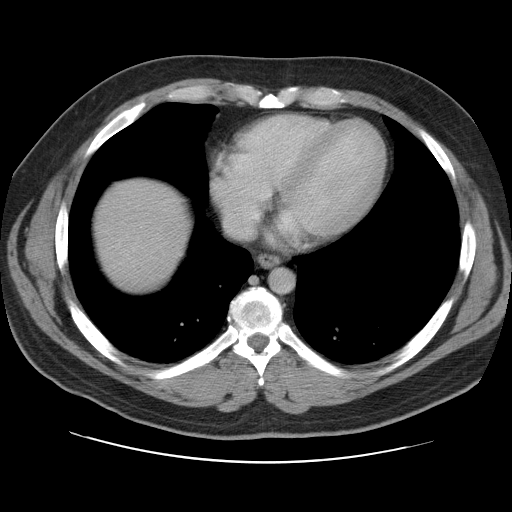
Contrast-enhanced abdominal CT, one axial slice; slice 103 of 109 in the series (ordered by position); 120 kVp; intravenous contrast given; soft-tissue window (W 400 / L 40 HU); 512 × 512 image matrix, field of view 402 × 402 mm. Male patient, age 35 years. From the clinical record (not read from this slice): diagnosis: colorectal cancer liver metastases, imaged before liver resection; multiple liver metastases: yes; largest metastasis: 2.8 cm; disease in both lobes: yes.
Annotated regions visible in this slice (manually delineated by an expert):
- liver: bounding box <94,179,187,291> (left, top, right, bottom; pixels)
- planned liver remnant (the part of the liver to remain after resection): <93,179,187,291>